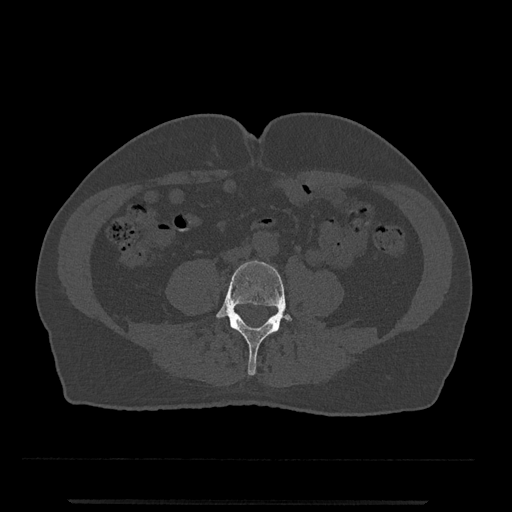
CT including the spine, one axial slice; slice 135 of 797 in the series (ordered by position); 120 kVp; bone window (W 1800 / L 400 HU); 0.5 mm slice thickness; 512 × 512 image matrix, field of view 419 × 419 mm. Patient: male, 63 years. Case-level facts recorded for this patient, not image findings: primary cancer: prostate.
Annotated regions visible in this slice (semi-automatic segmentation, software-assisted and operator-edited):
- L4 vertebra: box from (x=214, y=260) to (x=293, y=376) px